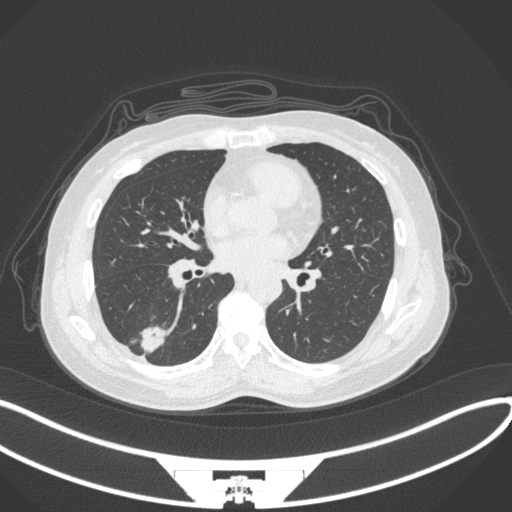
Chest CT, one axial slice. Slice 138 of 352 in the series (ordered by position). Reconstruction kernel B31f. 120 kVp. Lung window (W 1500 / L -600 HU). 1 mm slice thickness. 512 × 512 image matrix. Female patient, age 55 years. From the clinical record (not read from this slice): clinical TNM (as recorded): T1c N1 M0.
Annotated regions visible in this slice (bounding box drawn by a radiologist):
- lung tumour (recorded histology: adenocarcinoma): bounding box <138,325,170,356> (left, top, right, bottom; pixels)